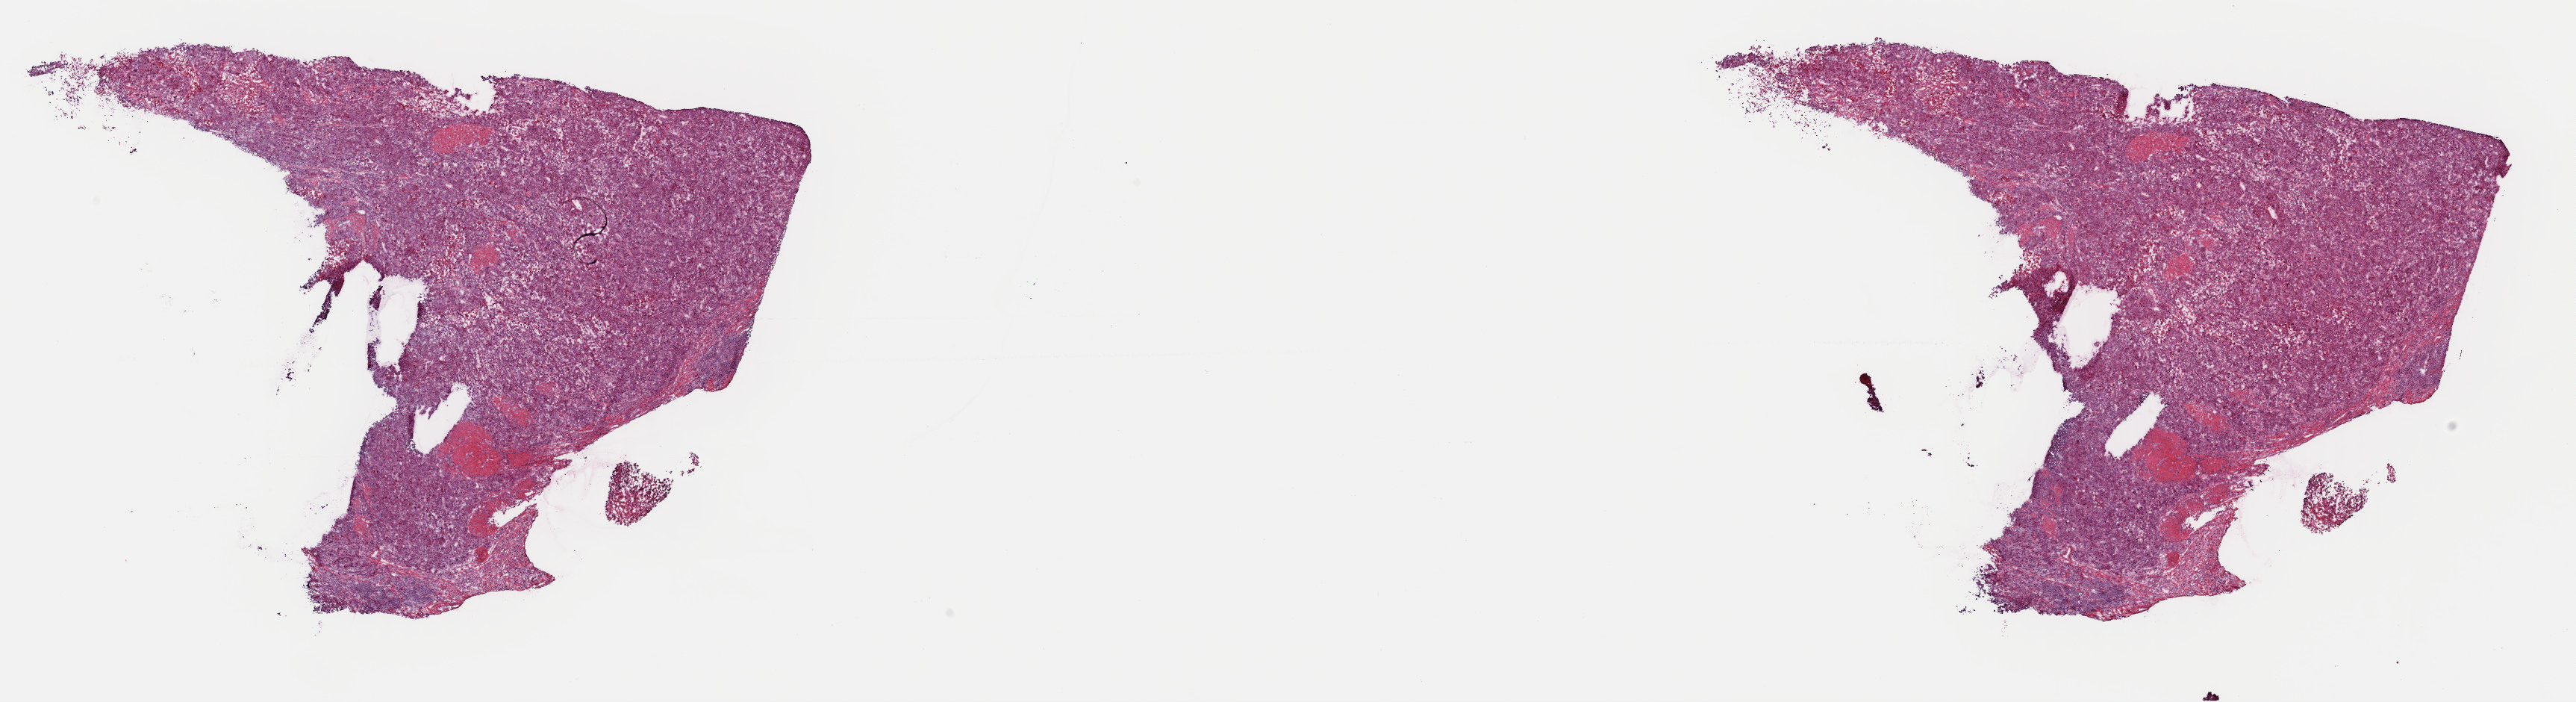
Digitized H&E tissue section (whole slide), whole scanned area (about 27.3 x 7.4 mm) shown as a low-resolution overview. Frozen section from the top of the tissue portion. Bladder, primary tumour sample. Male patient; age at initial diagnosis 70 years. Histologic grade: high grade. Pathologist review of this section (percent, as recorded): tumour cells 90%, tumour nuclei 75%, normal cells 0%, stromal cells 0%, necrosis 10%. Inflammatory infiltration, as recorded: lymphocyte infiltration 2%, monocyte infiltration 0%, neutrophil infiltration 0%.
• AJCC pathologic stage: II (7th edition)
• pathologic diagnosis: Transitional cell carcinoma
• TNM: T2a N0 MX